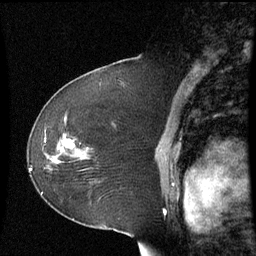
Breast MRI (dynamic contrast-enhanced), one sagittal slice; slice 38 of 60 in the series (ordered by position); dynamic contrast-enhanced series, image 2 of 3 at this slice position (ordered by acquisition); 1.5 T; TE 4.2 ms, TR 8.9 ms; 2.3 mm slice thickness; 256 × 256 image matrix, field of view 210 × 210 mm. Female patient, age 51 years. Case-level facts recorded for this patient, not image findings: setting: breast cancer imaged before/during neoadjuvant chemotherapy; receptor status: HR-positive, HER2-negative.
Annotated regions visible in this slice (semi-automatically segmented with operator editing):
- analysis volume of interest (the breast-tissue region the enhancement analysis was run in; not a lesion): bounding box (x1, y1, x2, y2) in pixels: (50, 117, 90, 174)
- tumour enhancement mask (voxels above the 70 % enhancement threshold inside the analysis volume of interest): (64, 140, 76, 149)